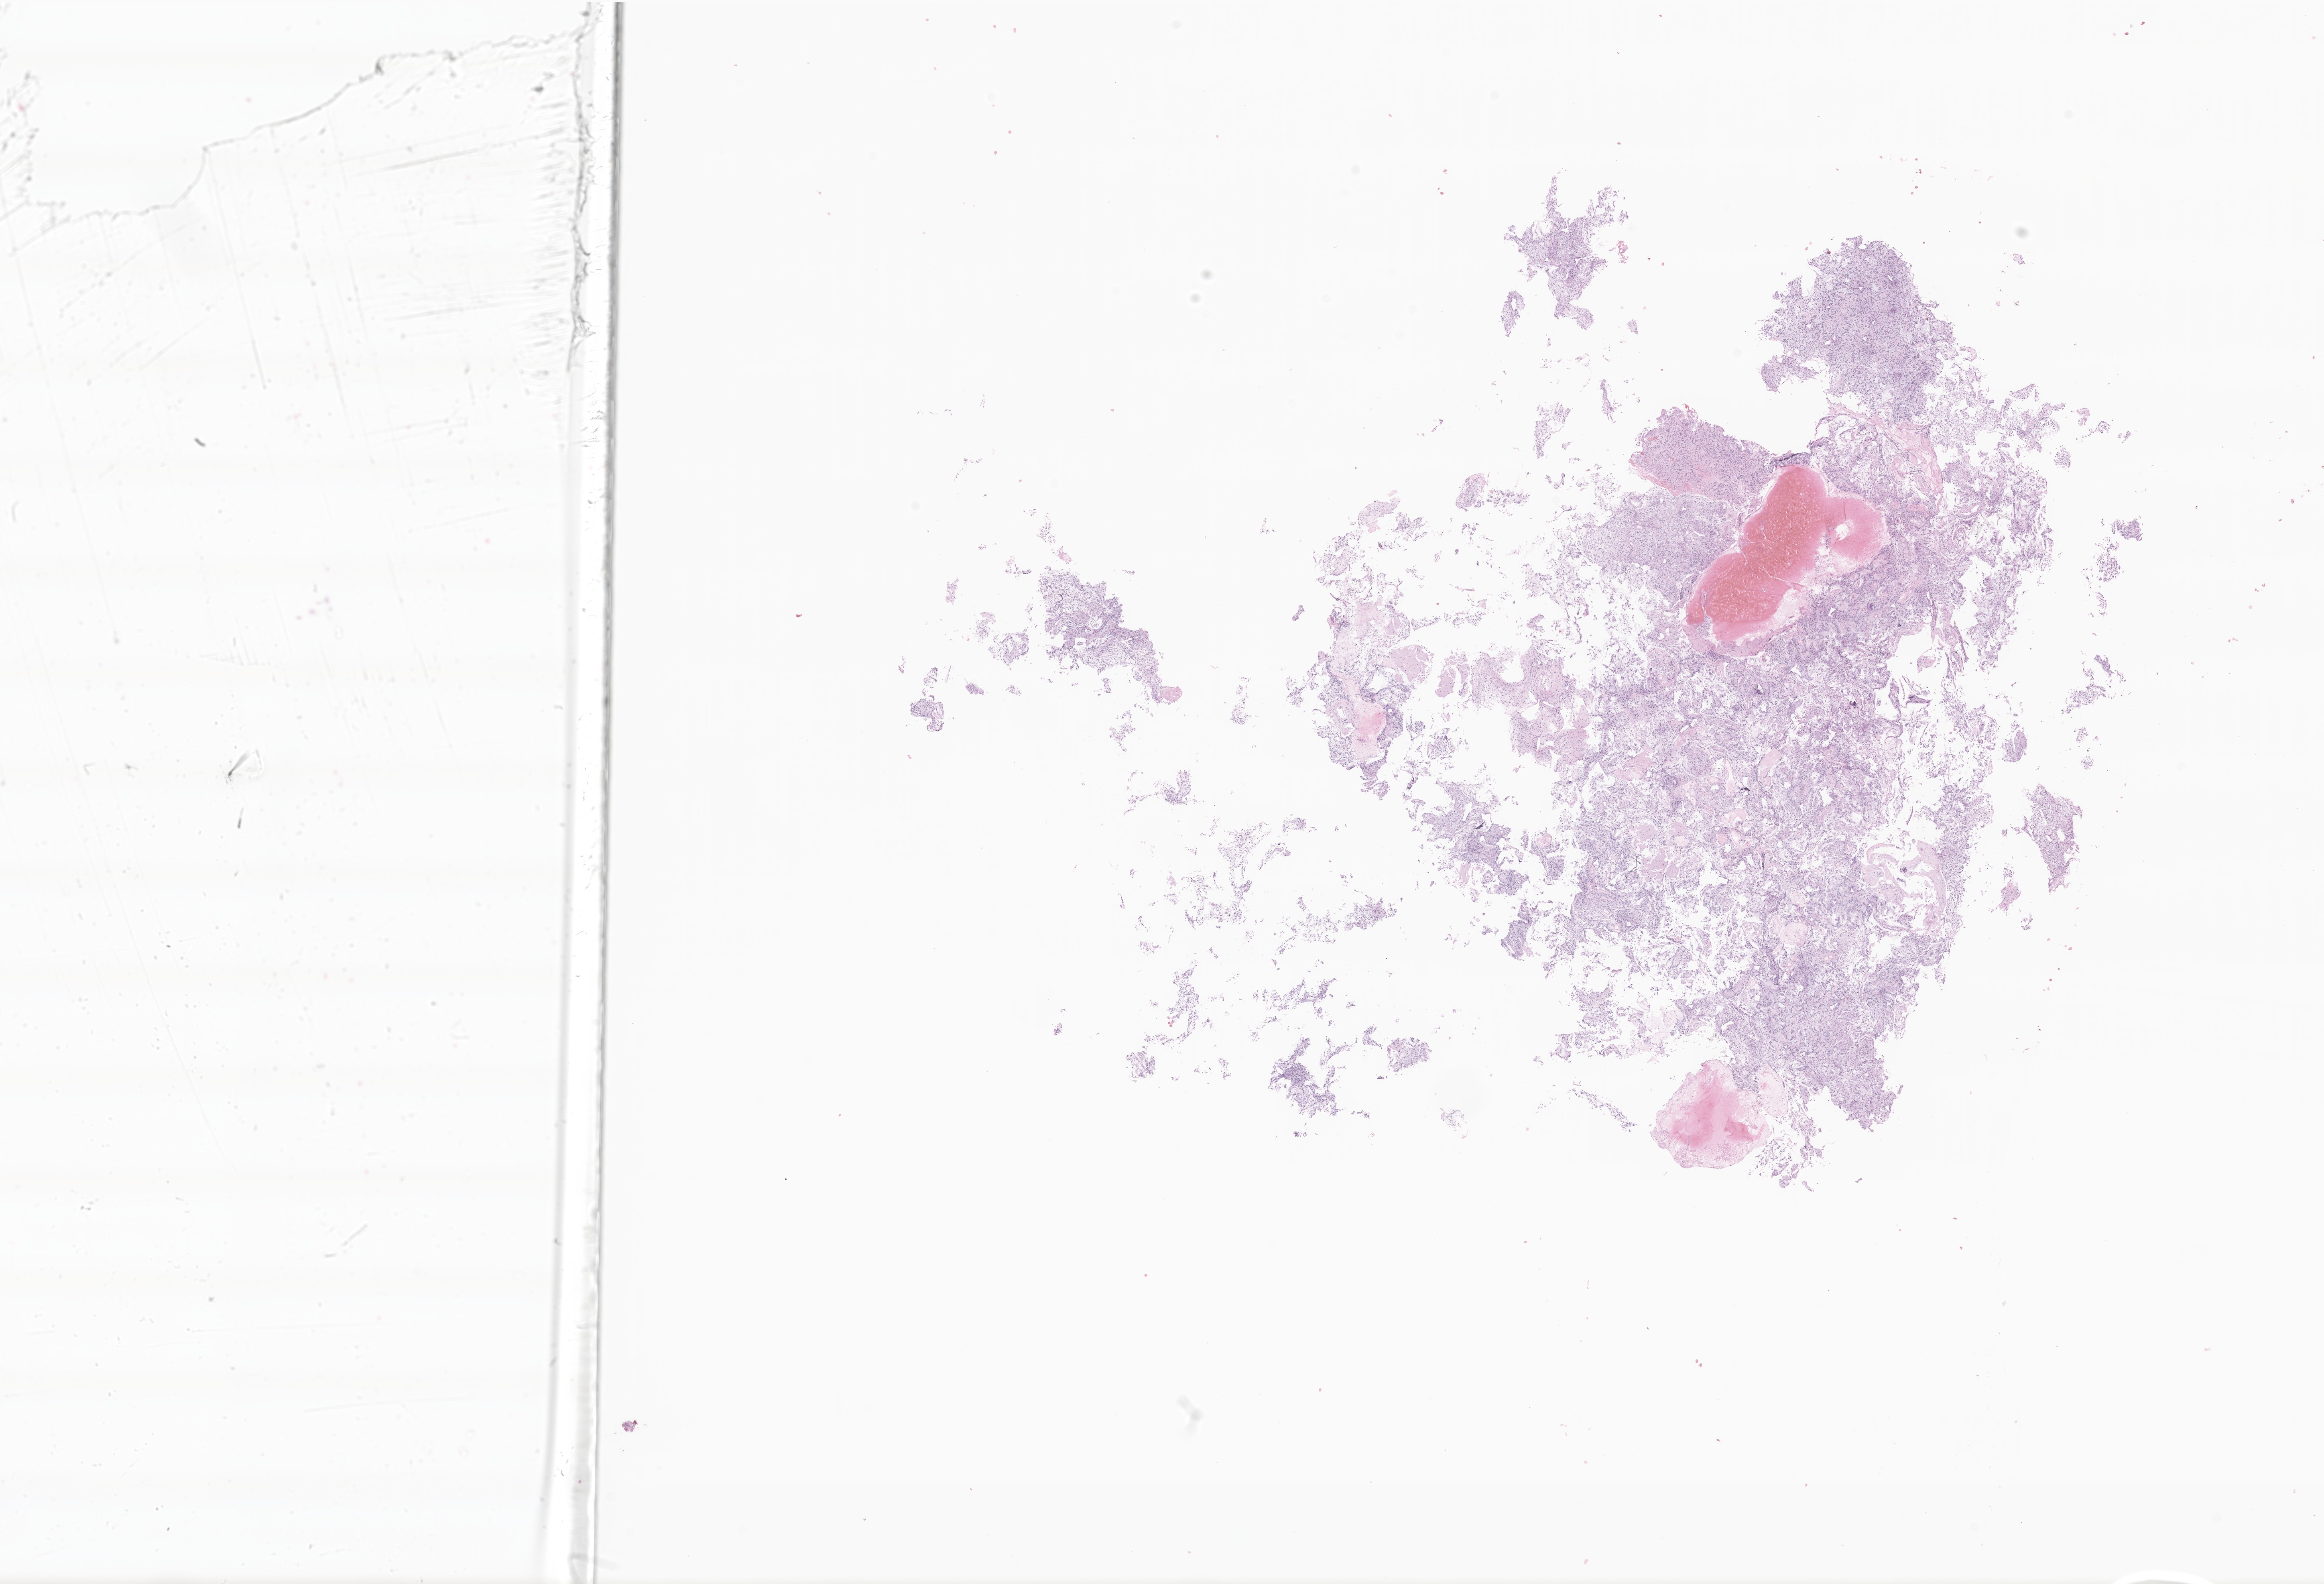
Whole-slide image, H&E stain of tumor tissue from the cerebral ventricle — whole scanned area (about 24.4 x 16.6 mm) shown as a low-resolution overview. Formalin-fixed, paraffin-embedded (FFPE) tissue. Patient: male, age 202 months (16 years 10 months).
Diagnosis: Pilocytic astrocytoma.